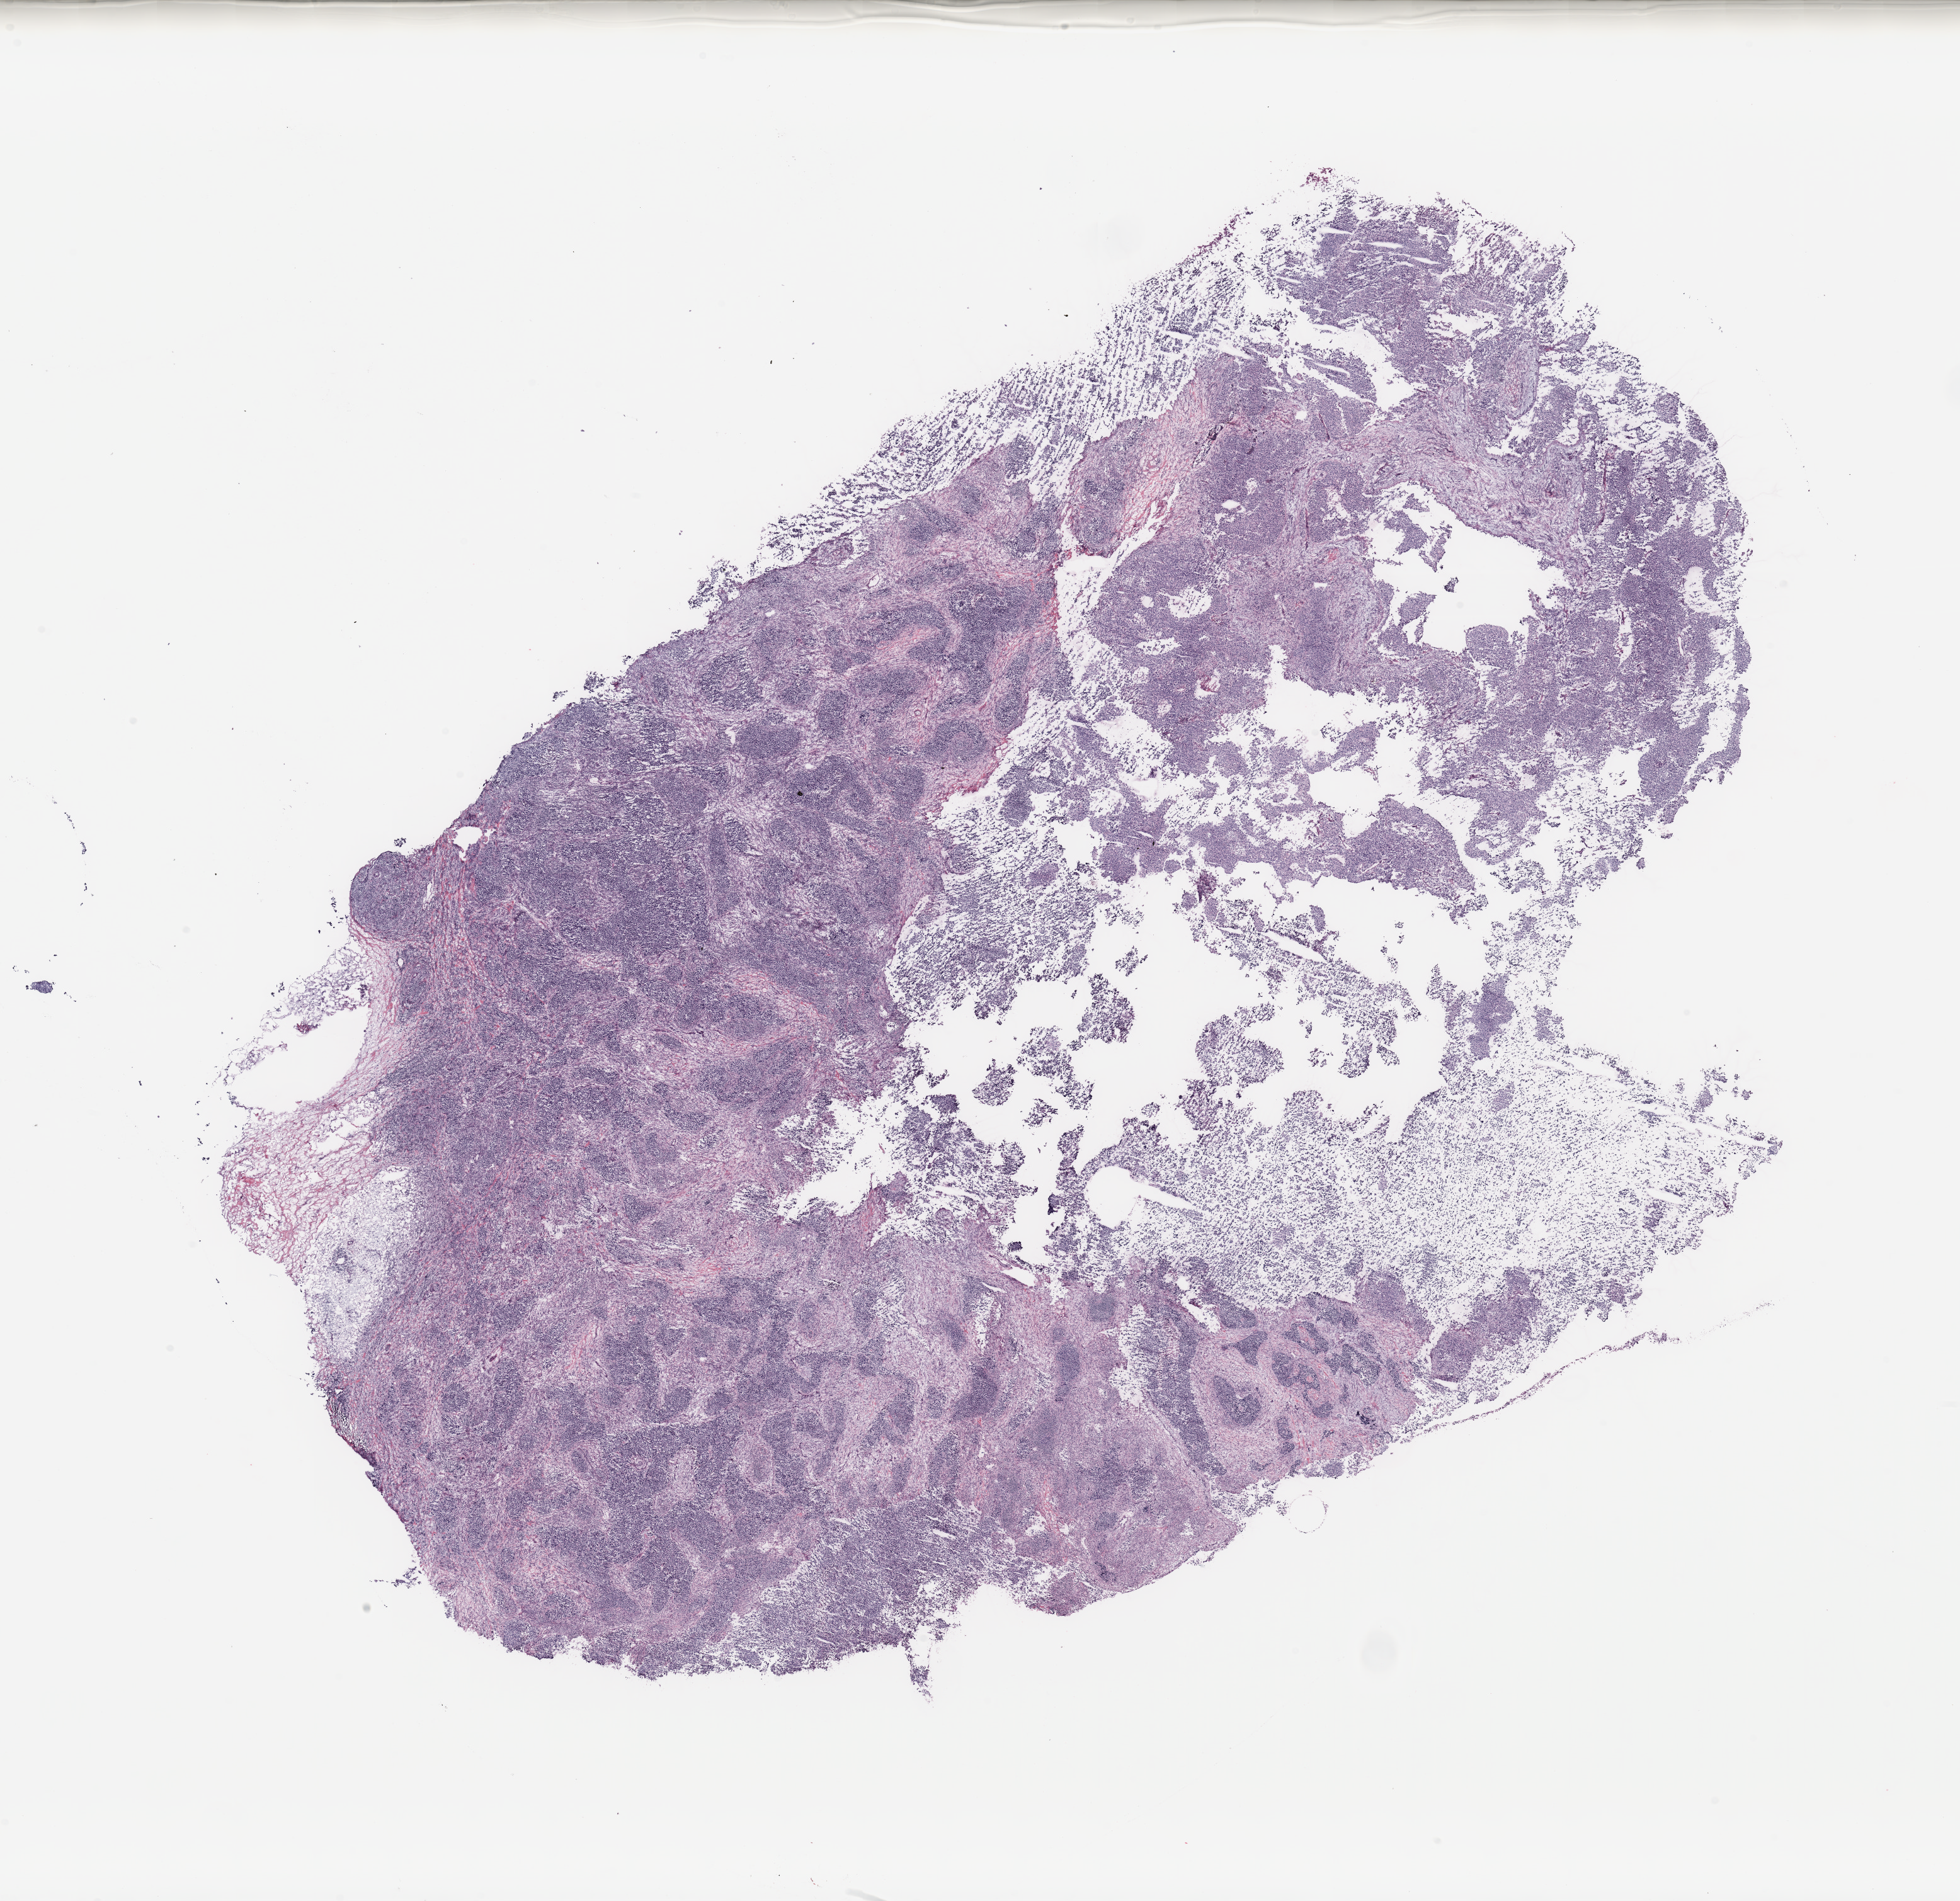
H&E whole-slide image — a low-resolution overview of the entire scanned area, about 24.6 x 23.9 mm (slide scanned at 20x); breast, tumour tissue. Female, 80 y/o.
Diagnosis: Infiltrating duct carcinoma, NOS. AJCC pathologic stage: IIA.